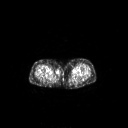
FDG PET of an extremity soft-tissue mass (from a PET/CT study), one axial slice. Position 226 of 311 along the scan axis. 3.27 mm slice thickness. 128 × 128 image matrix. Female patient, age 78 years. Case-level facts recorded for this patient, not image findings: histological type: leiomyosarcoma; grade: intermediate; site of the primary tumour: parascapusular.
Outlined on this slice (expert contour drawn on MRI and transferred to this co-registered scan by the dataset authors):
- gross tumour volume including surrounding oedema: box from (x=56, y=72) to (x=59, y=74) px